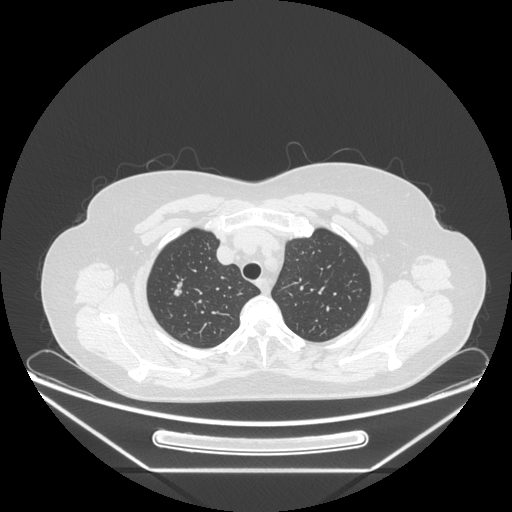
Chest CT, one axial slice. Slice 201 of 236 in the series (ordered by position). Reconstruction kernel STANDARD. 120 kVp. Lung window (W 1500 / L -600 HU). 1.25 mm slice thickness. 512 × 512 image matrix. Patient: female, 60 years. From the clinical record (not read from this slice): clinical TNM (as recorded): T1c N0 M0; histopathological grade: G2-3.
Structures marked on this image (rectangle marked by the reading radiologist):
- lung tumour (recorded histology: adenocarcinoma): box from (x=167, y=269) to (x=189, y=302) px